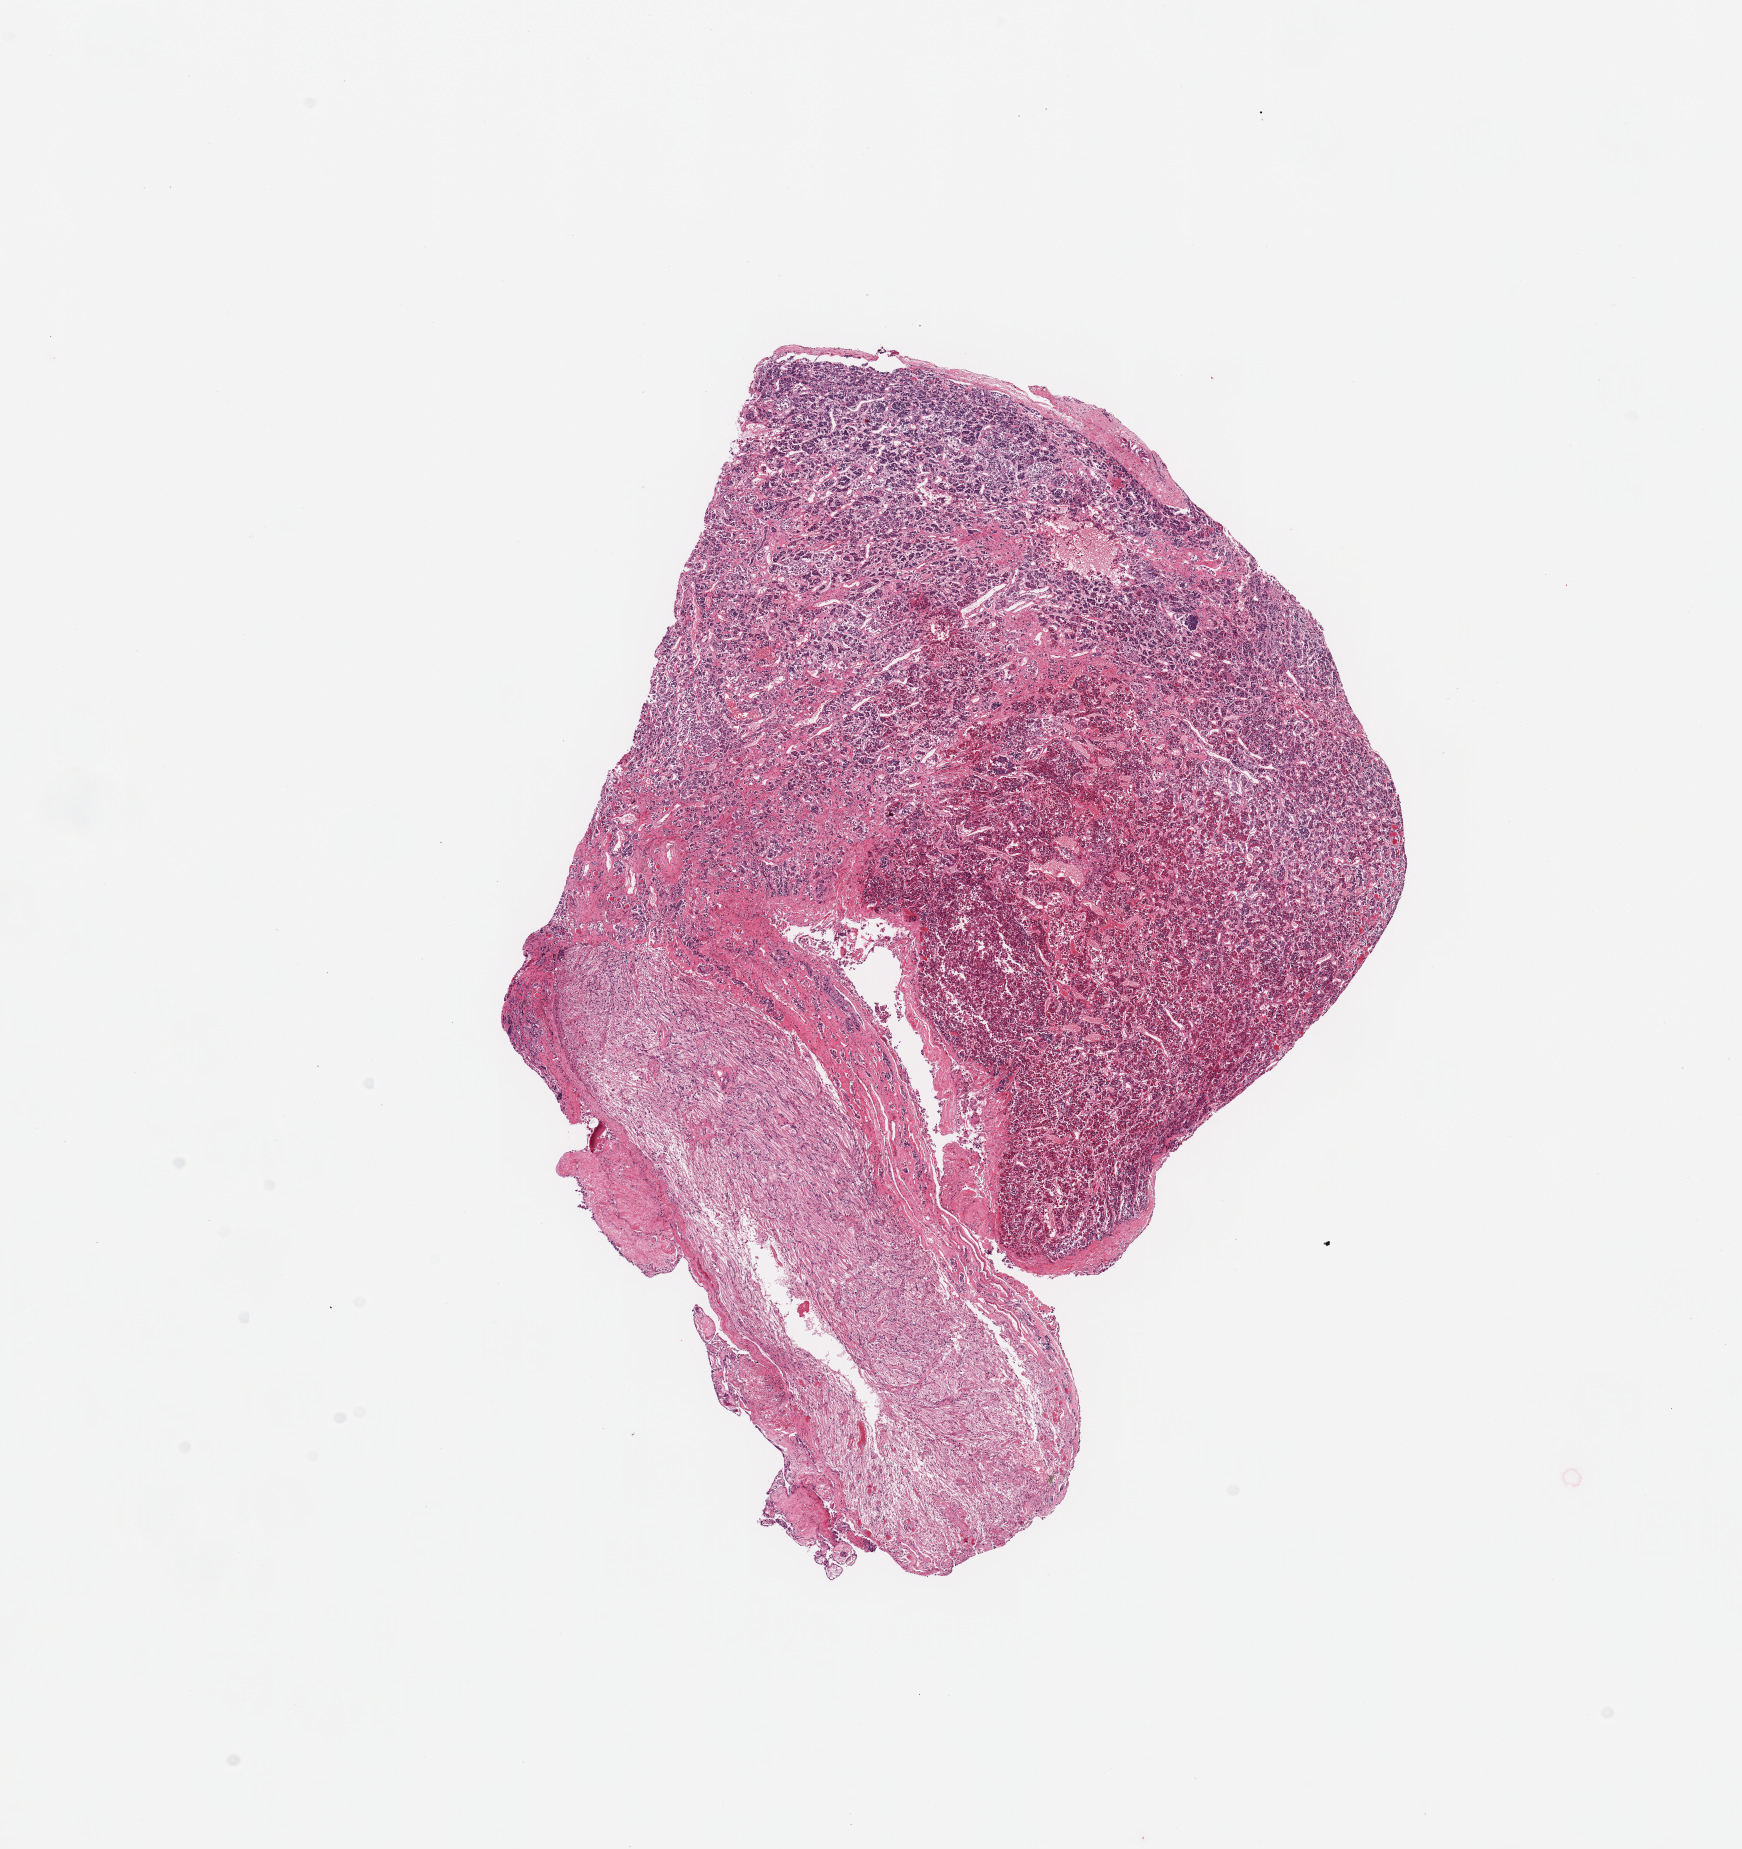
H&E whole-slide image — whole scanned area (about 13.8 x 14.6 mm, acquisition: 20x scan) shown as a low-resolution overview. PAXgene-fixed, paraffin-embedded tissue. Sampled site (target tissue): pituitary. Donor tissue sample. Male donor.
• reviewer comment on this tissue sample: 1 piece; adenohypophysis makes up 2/3 and is moderately autolyzed; neurohypophysis is better preserved